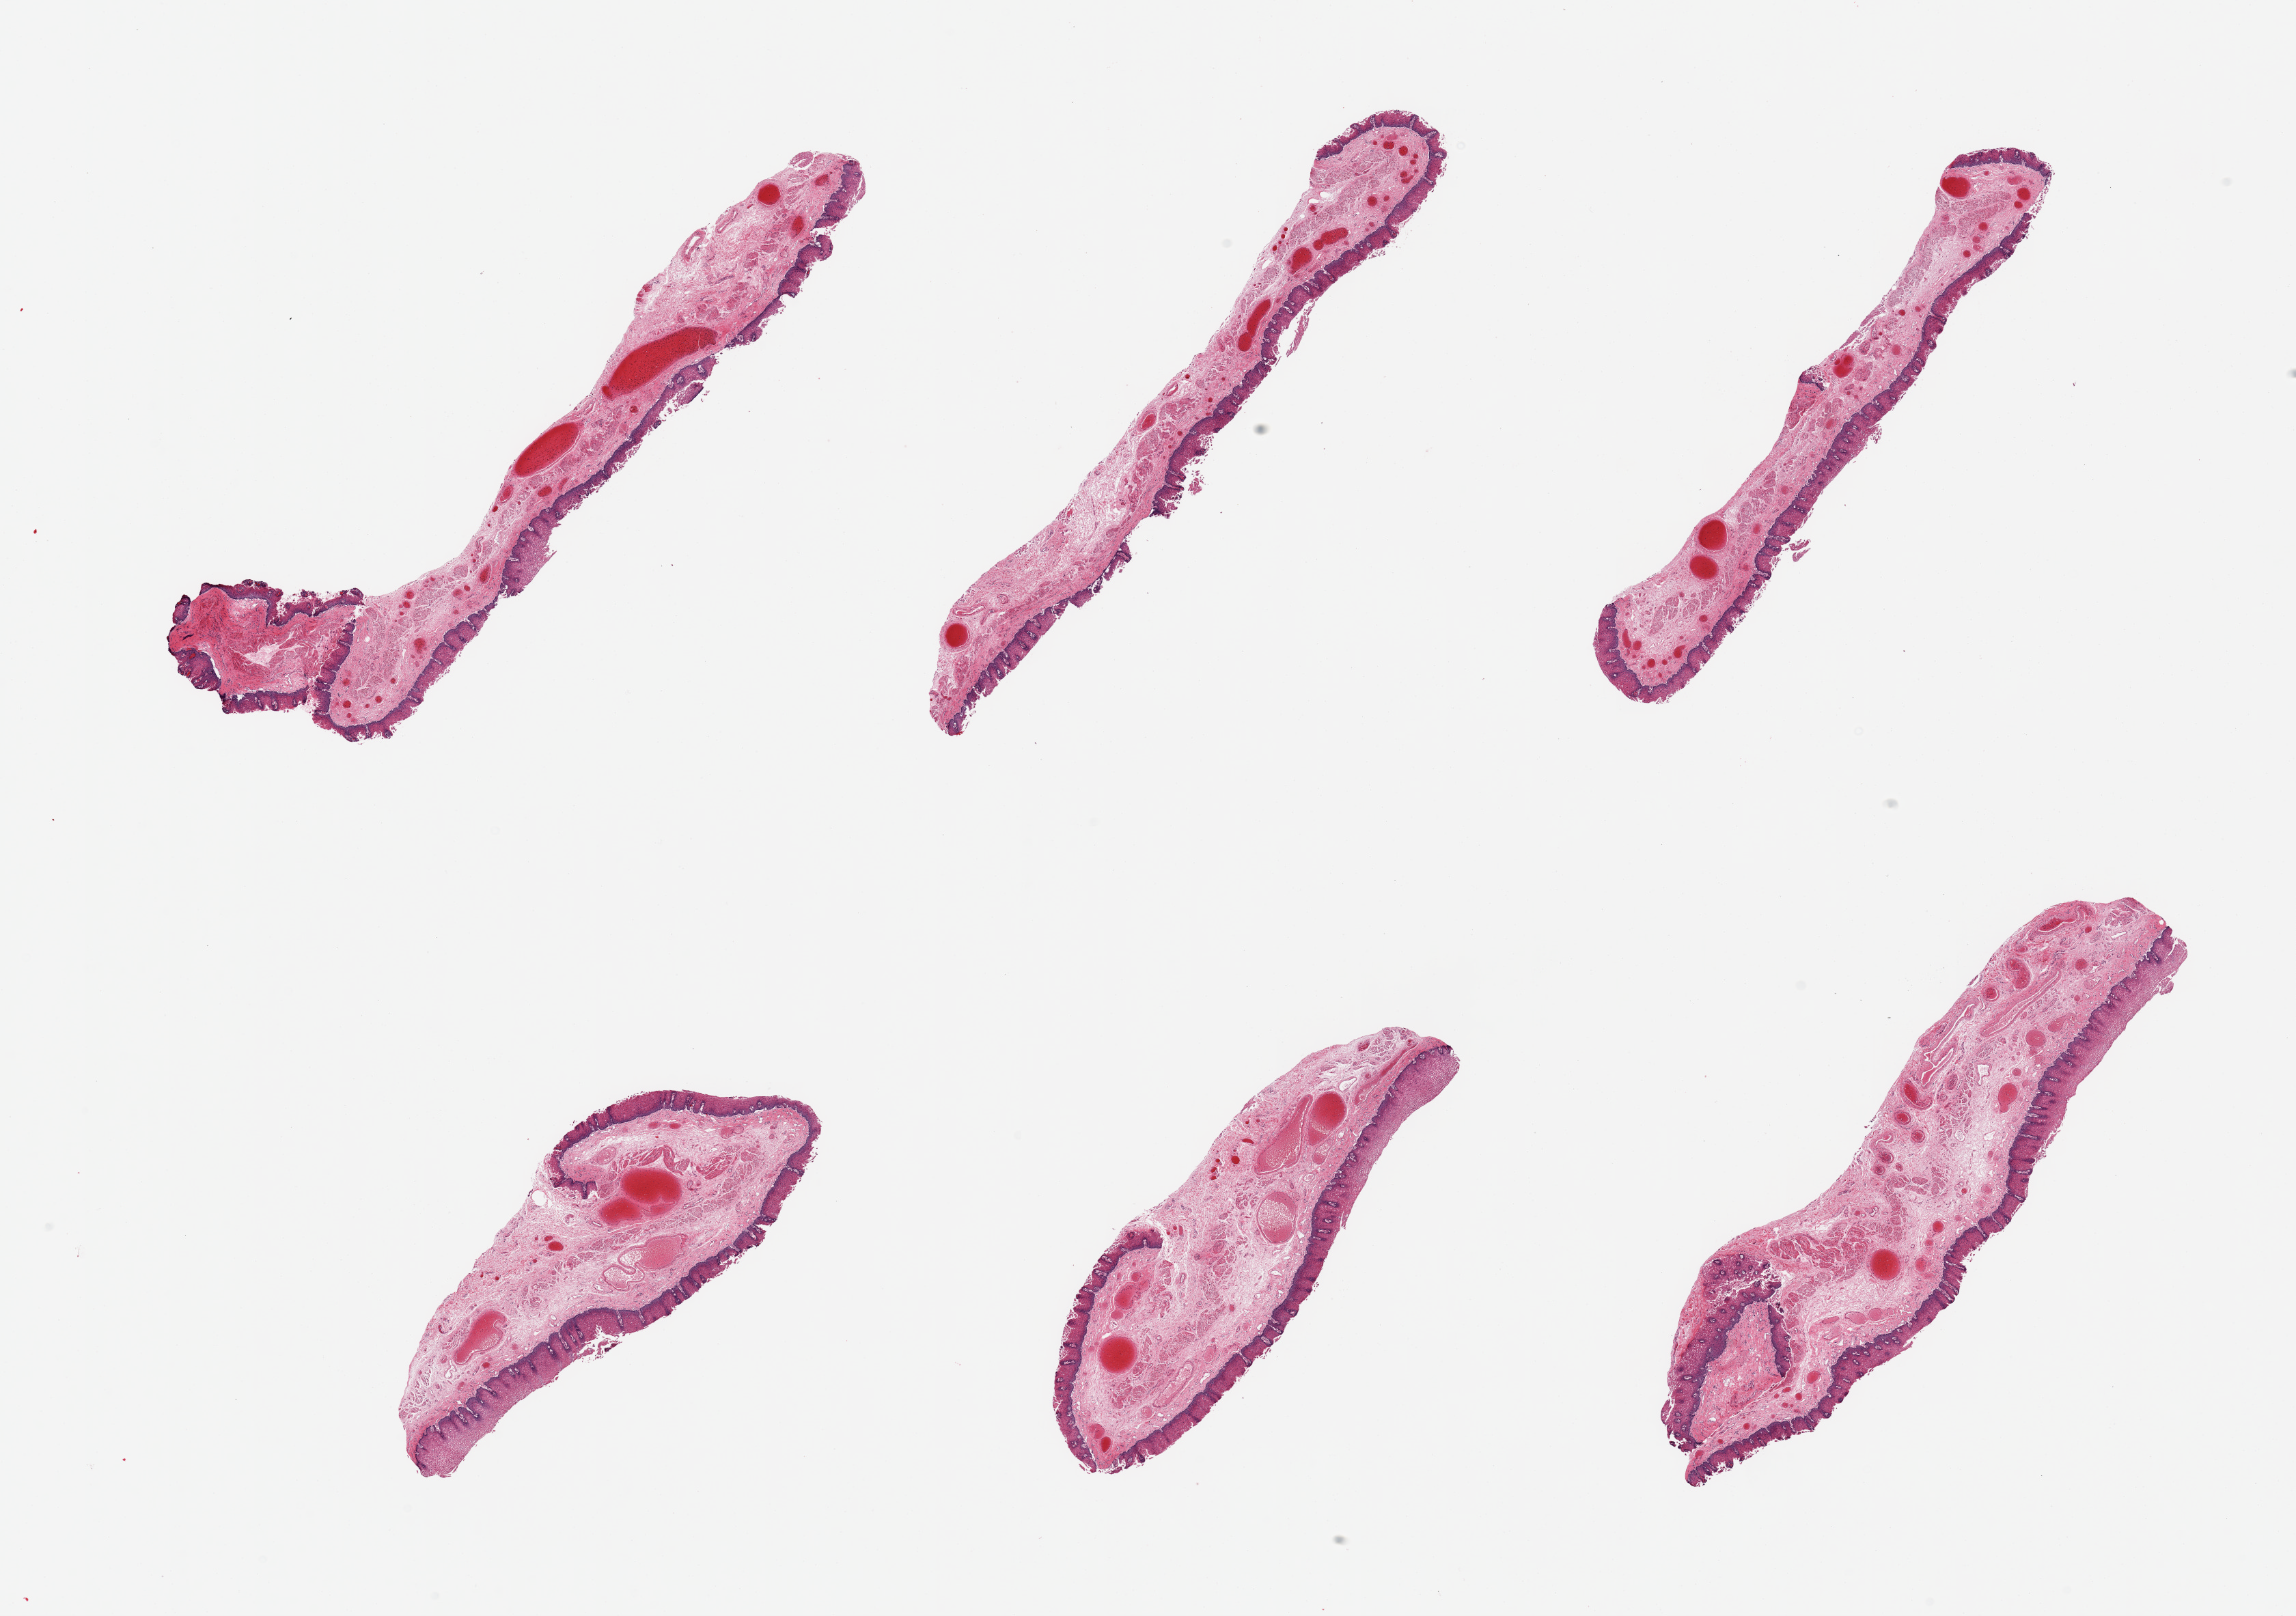
Digitized hematoxylin and eosin (H&E)-stained section — shown as a low-resolution overview of the whole scanned area (about 26.6 x 18.7 mm), PAXgene-fixed, paraffin-embedded tissue, section of esophageal mucous membrane (target tissue), tissue donor sample. Donor: male.
Pathologist's review note for this sample: 6 pieces, squamous mucosa beginning to slough, up to~0.3mm, 20-30% thickness.